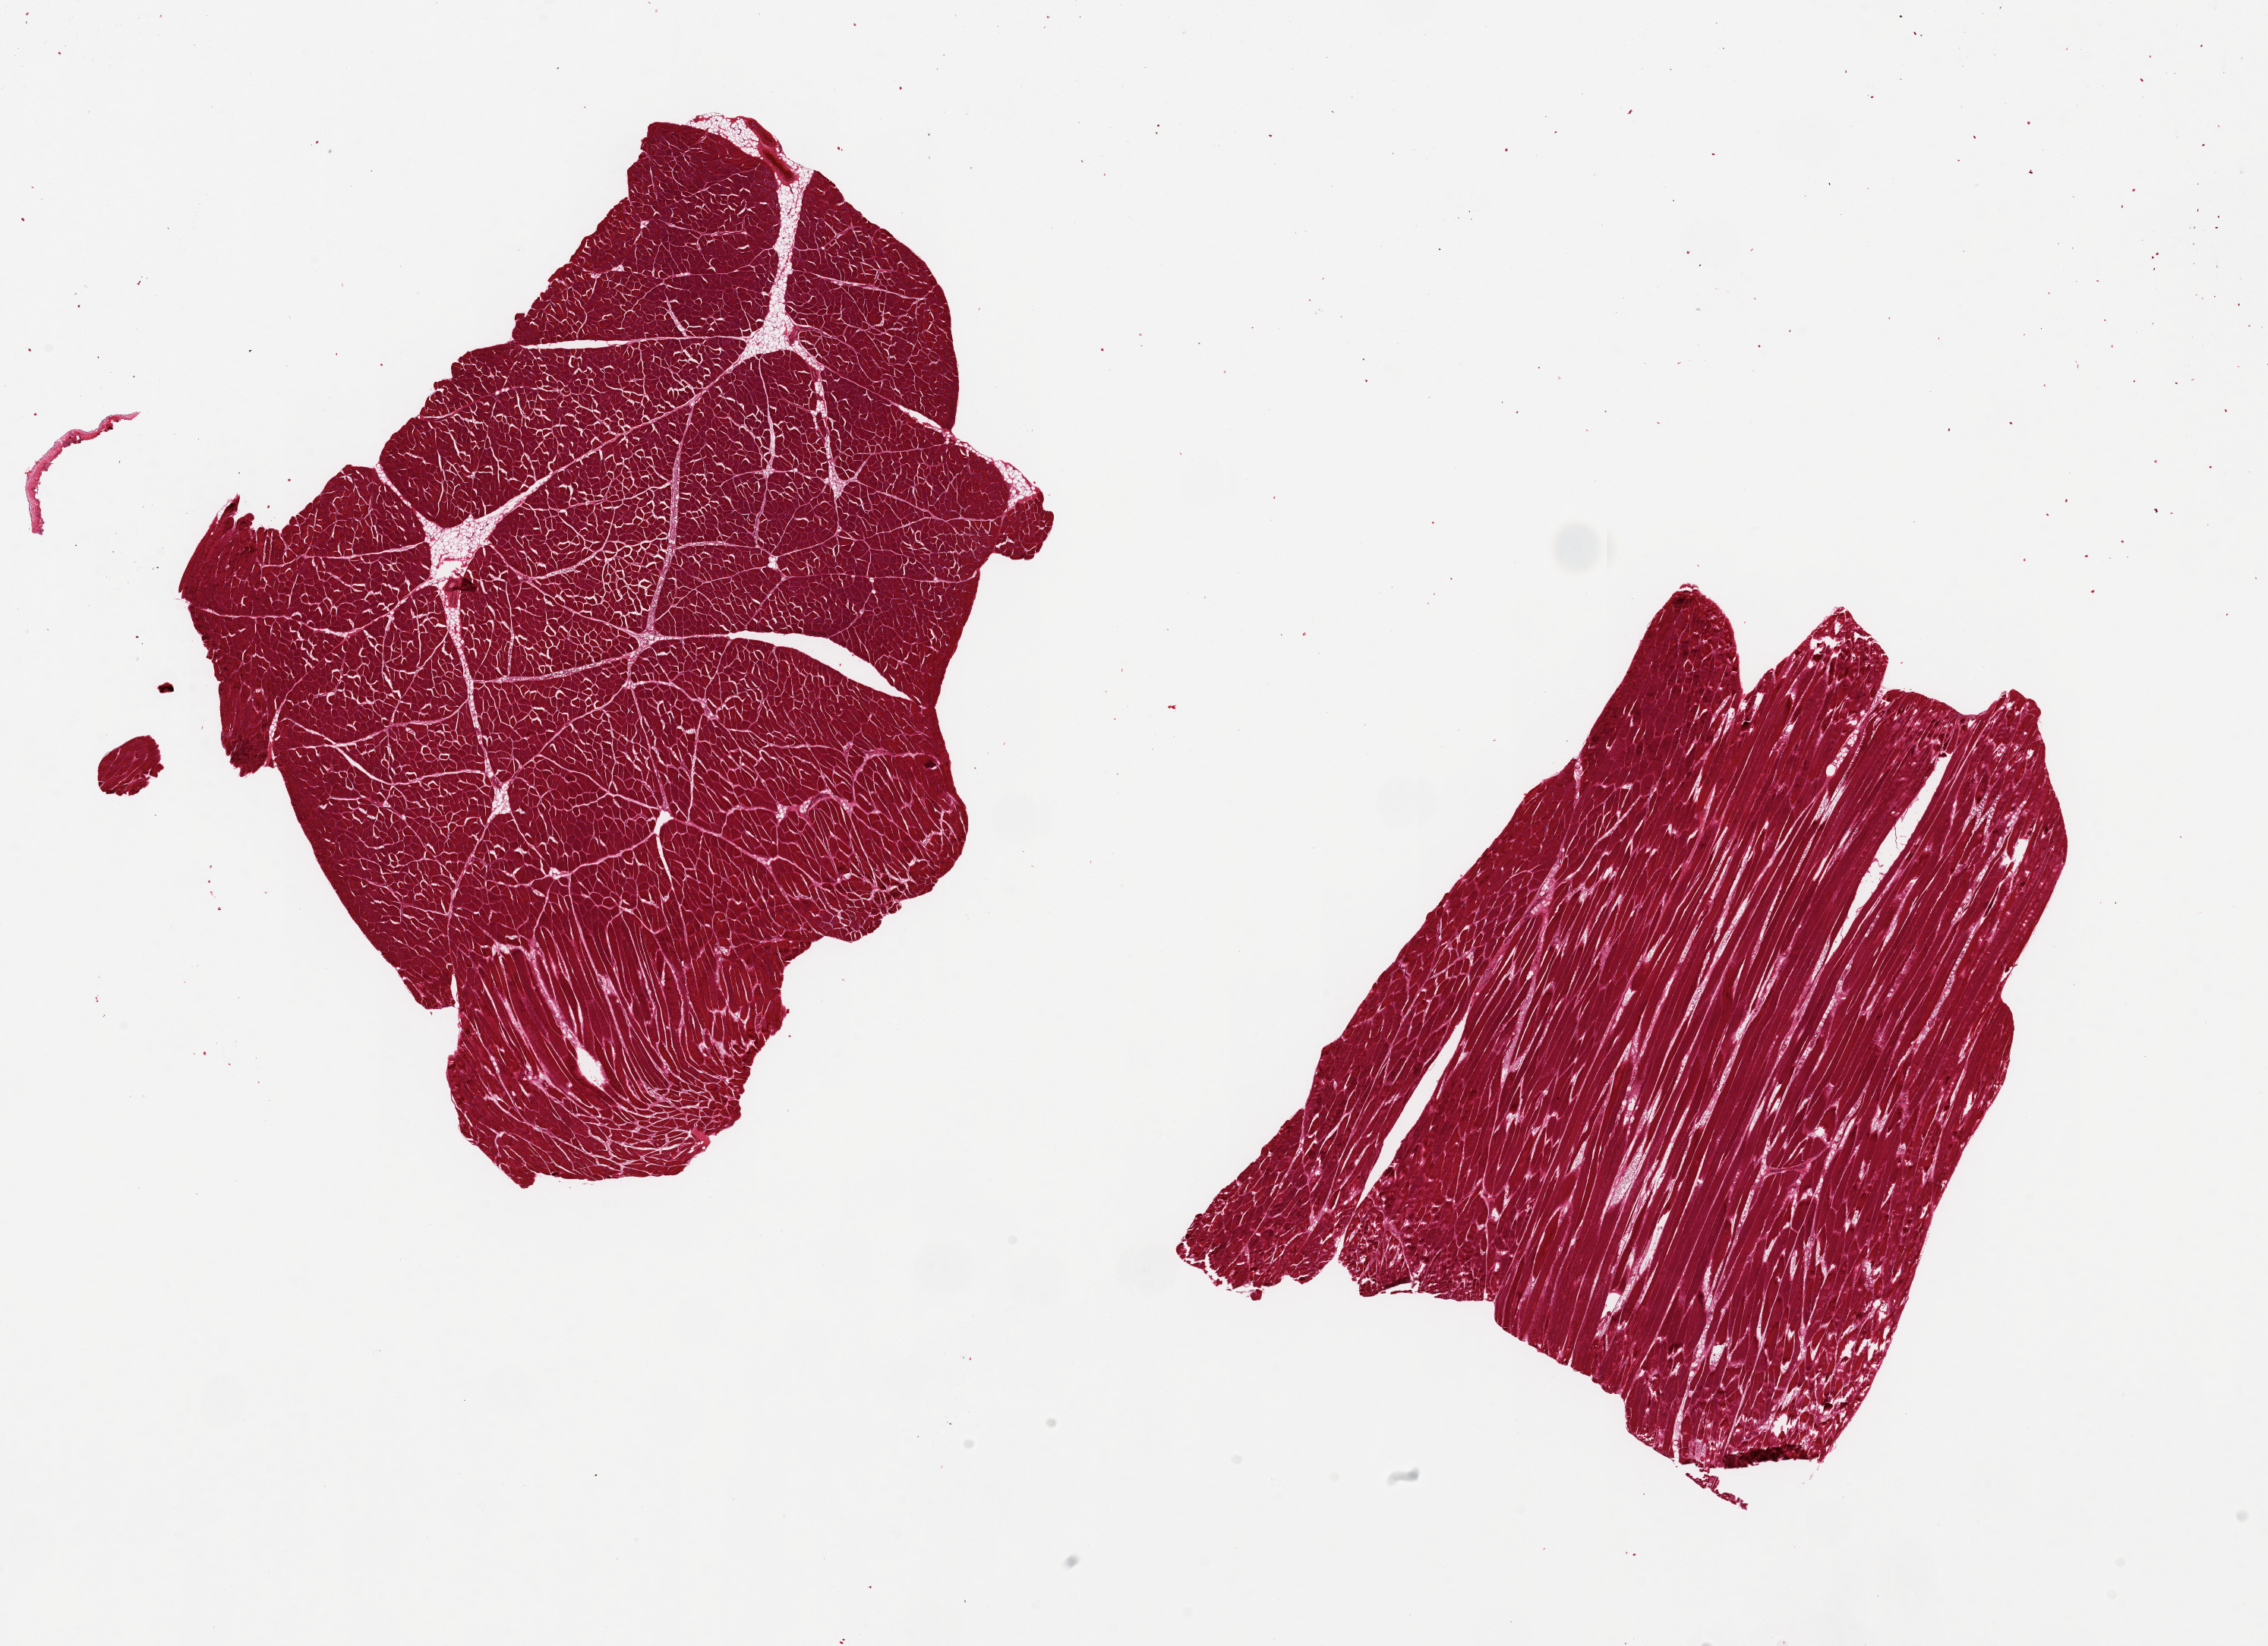
Digitized haematoxylin and eosin-stained section, low-resolution overview of the scanned area, about 23.6 x 17.1 mm. PAXgene-fixed paraffin-embedded (PFPE) section. Sampled site (target tissue): skeletal muscle. Donor tissue sample. Male donor.
Pathologist's review note for this sample: 2 pieces 9x8 & 9x6 mm; no adipose.